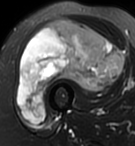
MRI of an extremity soft-tissue mass, one axial slice. Position 48 of 95 along the scan axis. T2-weighted fat-saturated. MR volume resampled by the dataset authors to the PET/CT grid (not the native acquisition matrix). 135 × 146 image matrix, field of view 132 × 143 mm. Female patient. Case-level facts recorded for this patient, not image findings: histological type: pleiomorphic undifferentiated sarcoma; grade: high; site of the primary tumour: right quadricep.
Annotated regions visible in this slice (expert contour drawn on MRI and transferred to this co-registered scan by the dataset authors):
- gross tumour volume including surrounding oedema: bounding box (x1, y1, x2, y2) in pixels: (18, 18, 125, 122)
- gross tumour volume (mass): (18, 18, 125, 122)